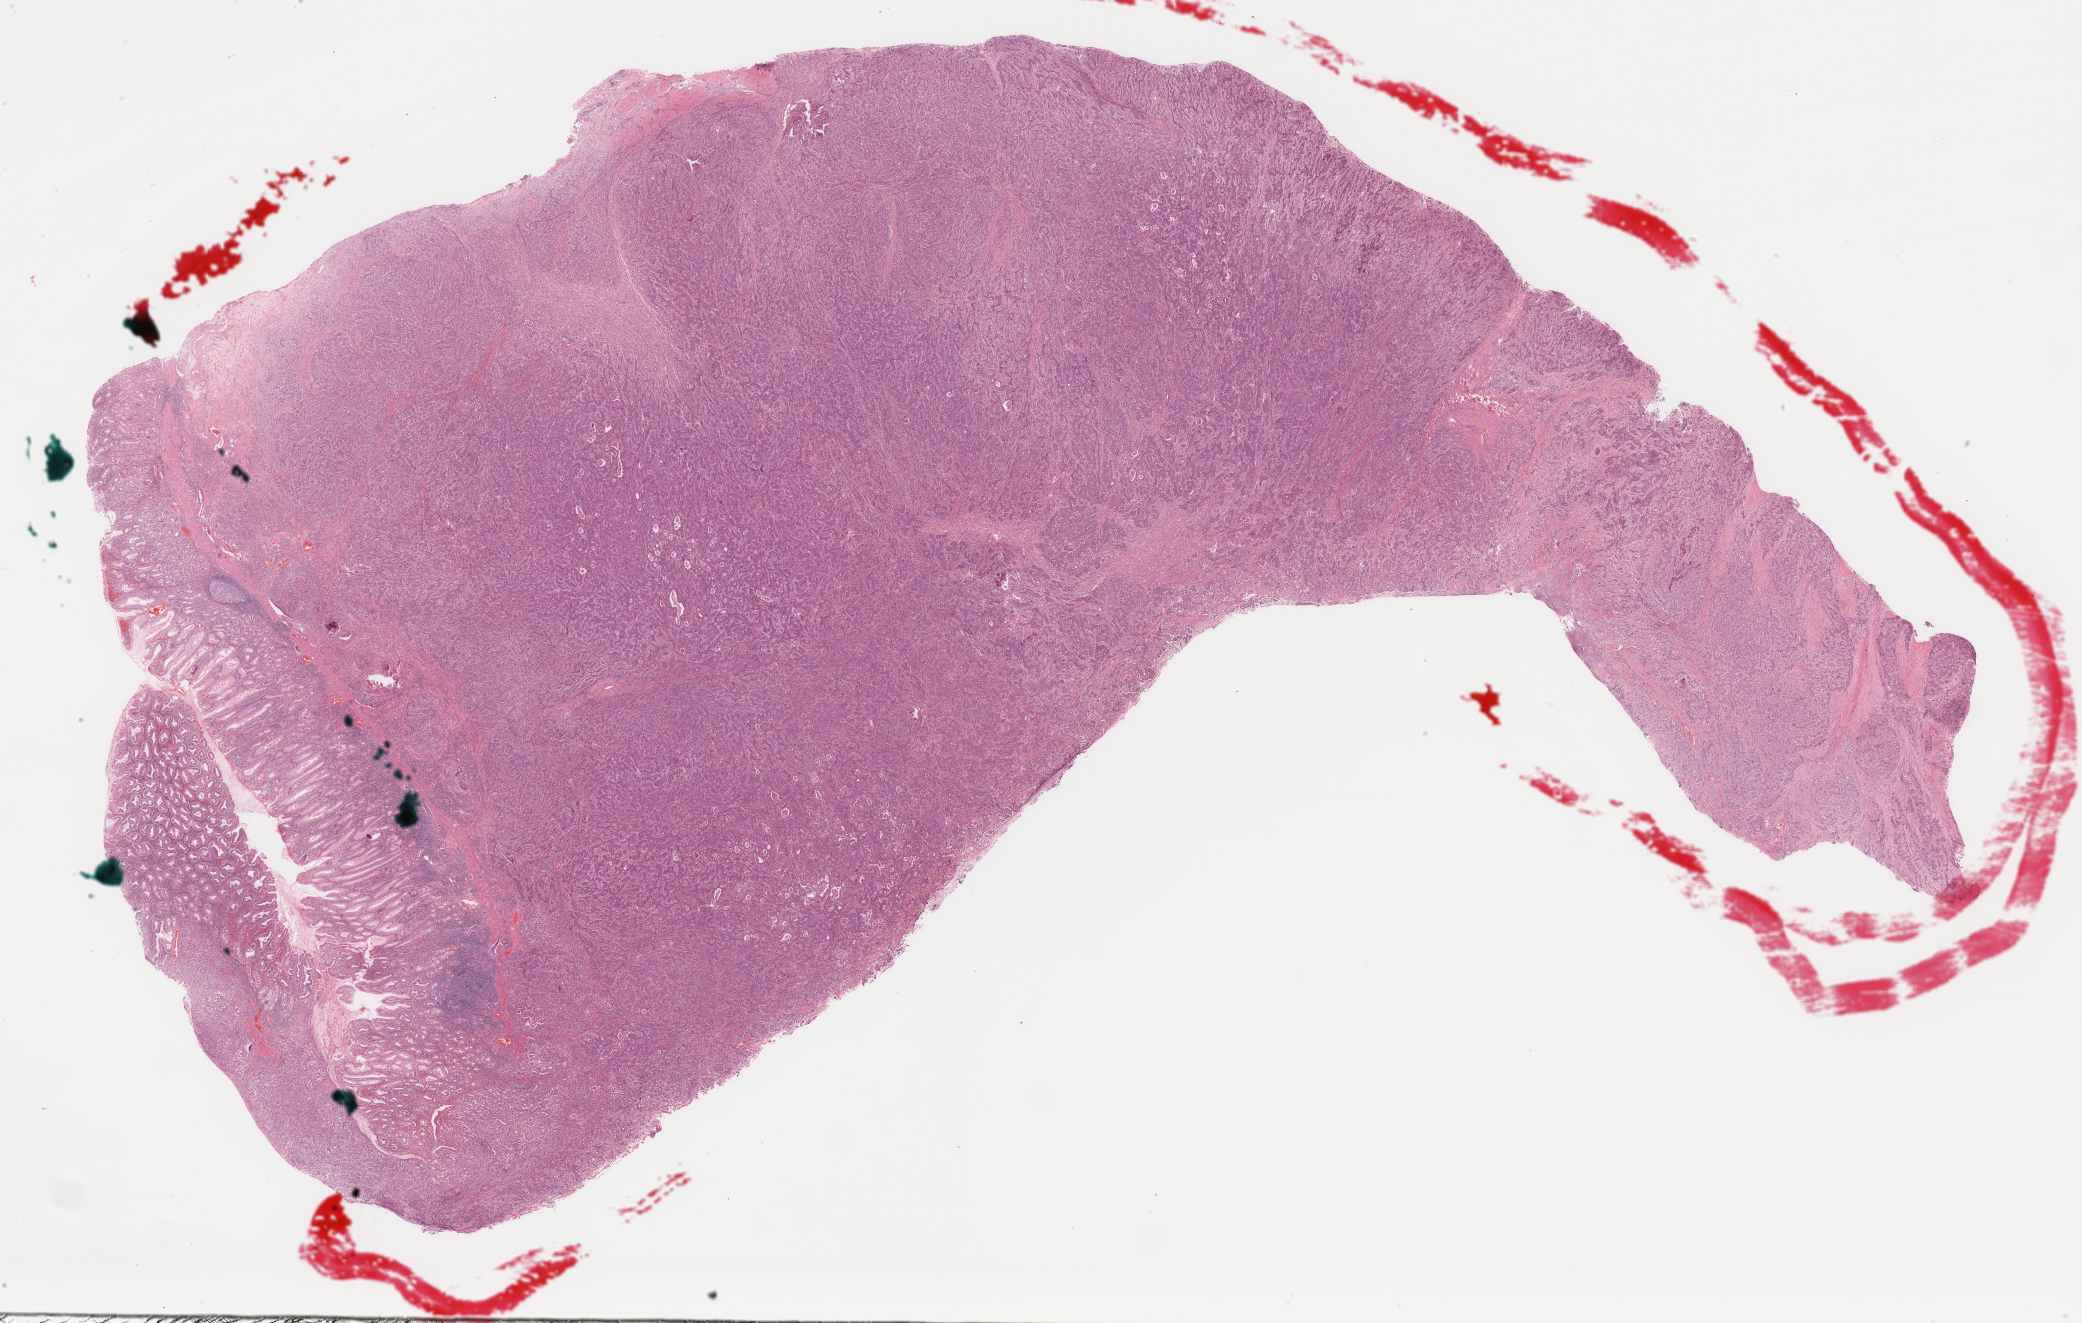
H&E whole-slide image, shown as a low-resolution overview of the whole scanned area (about 33.1 x 21.0 mm, acquisition: 40x scan); formalin-fixed paraffin-embedded (FFPE) diagnostic section; sample: primary tumour, stomach. Male patient; age at initial diagnosis 72 years. Histologic grade: G3 (poorly differentiated).
TNM: T4a N2 M0. Pathologic diagnosis: Adenocarcinoma, NOS. AJCC pathologic stage: IIIB. Lymph nodes positive (case pathology): 3 of 8 examined.